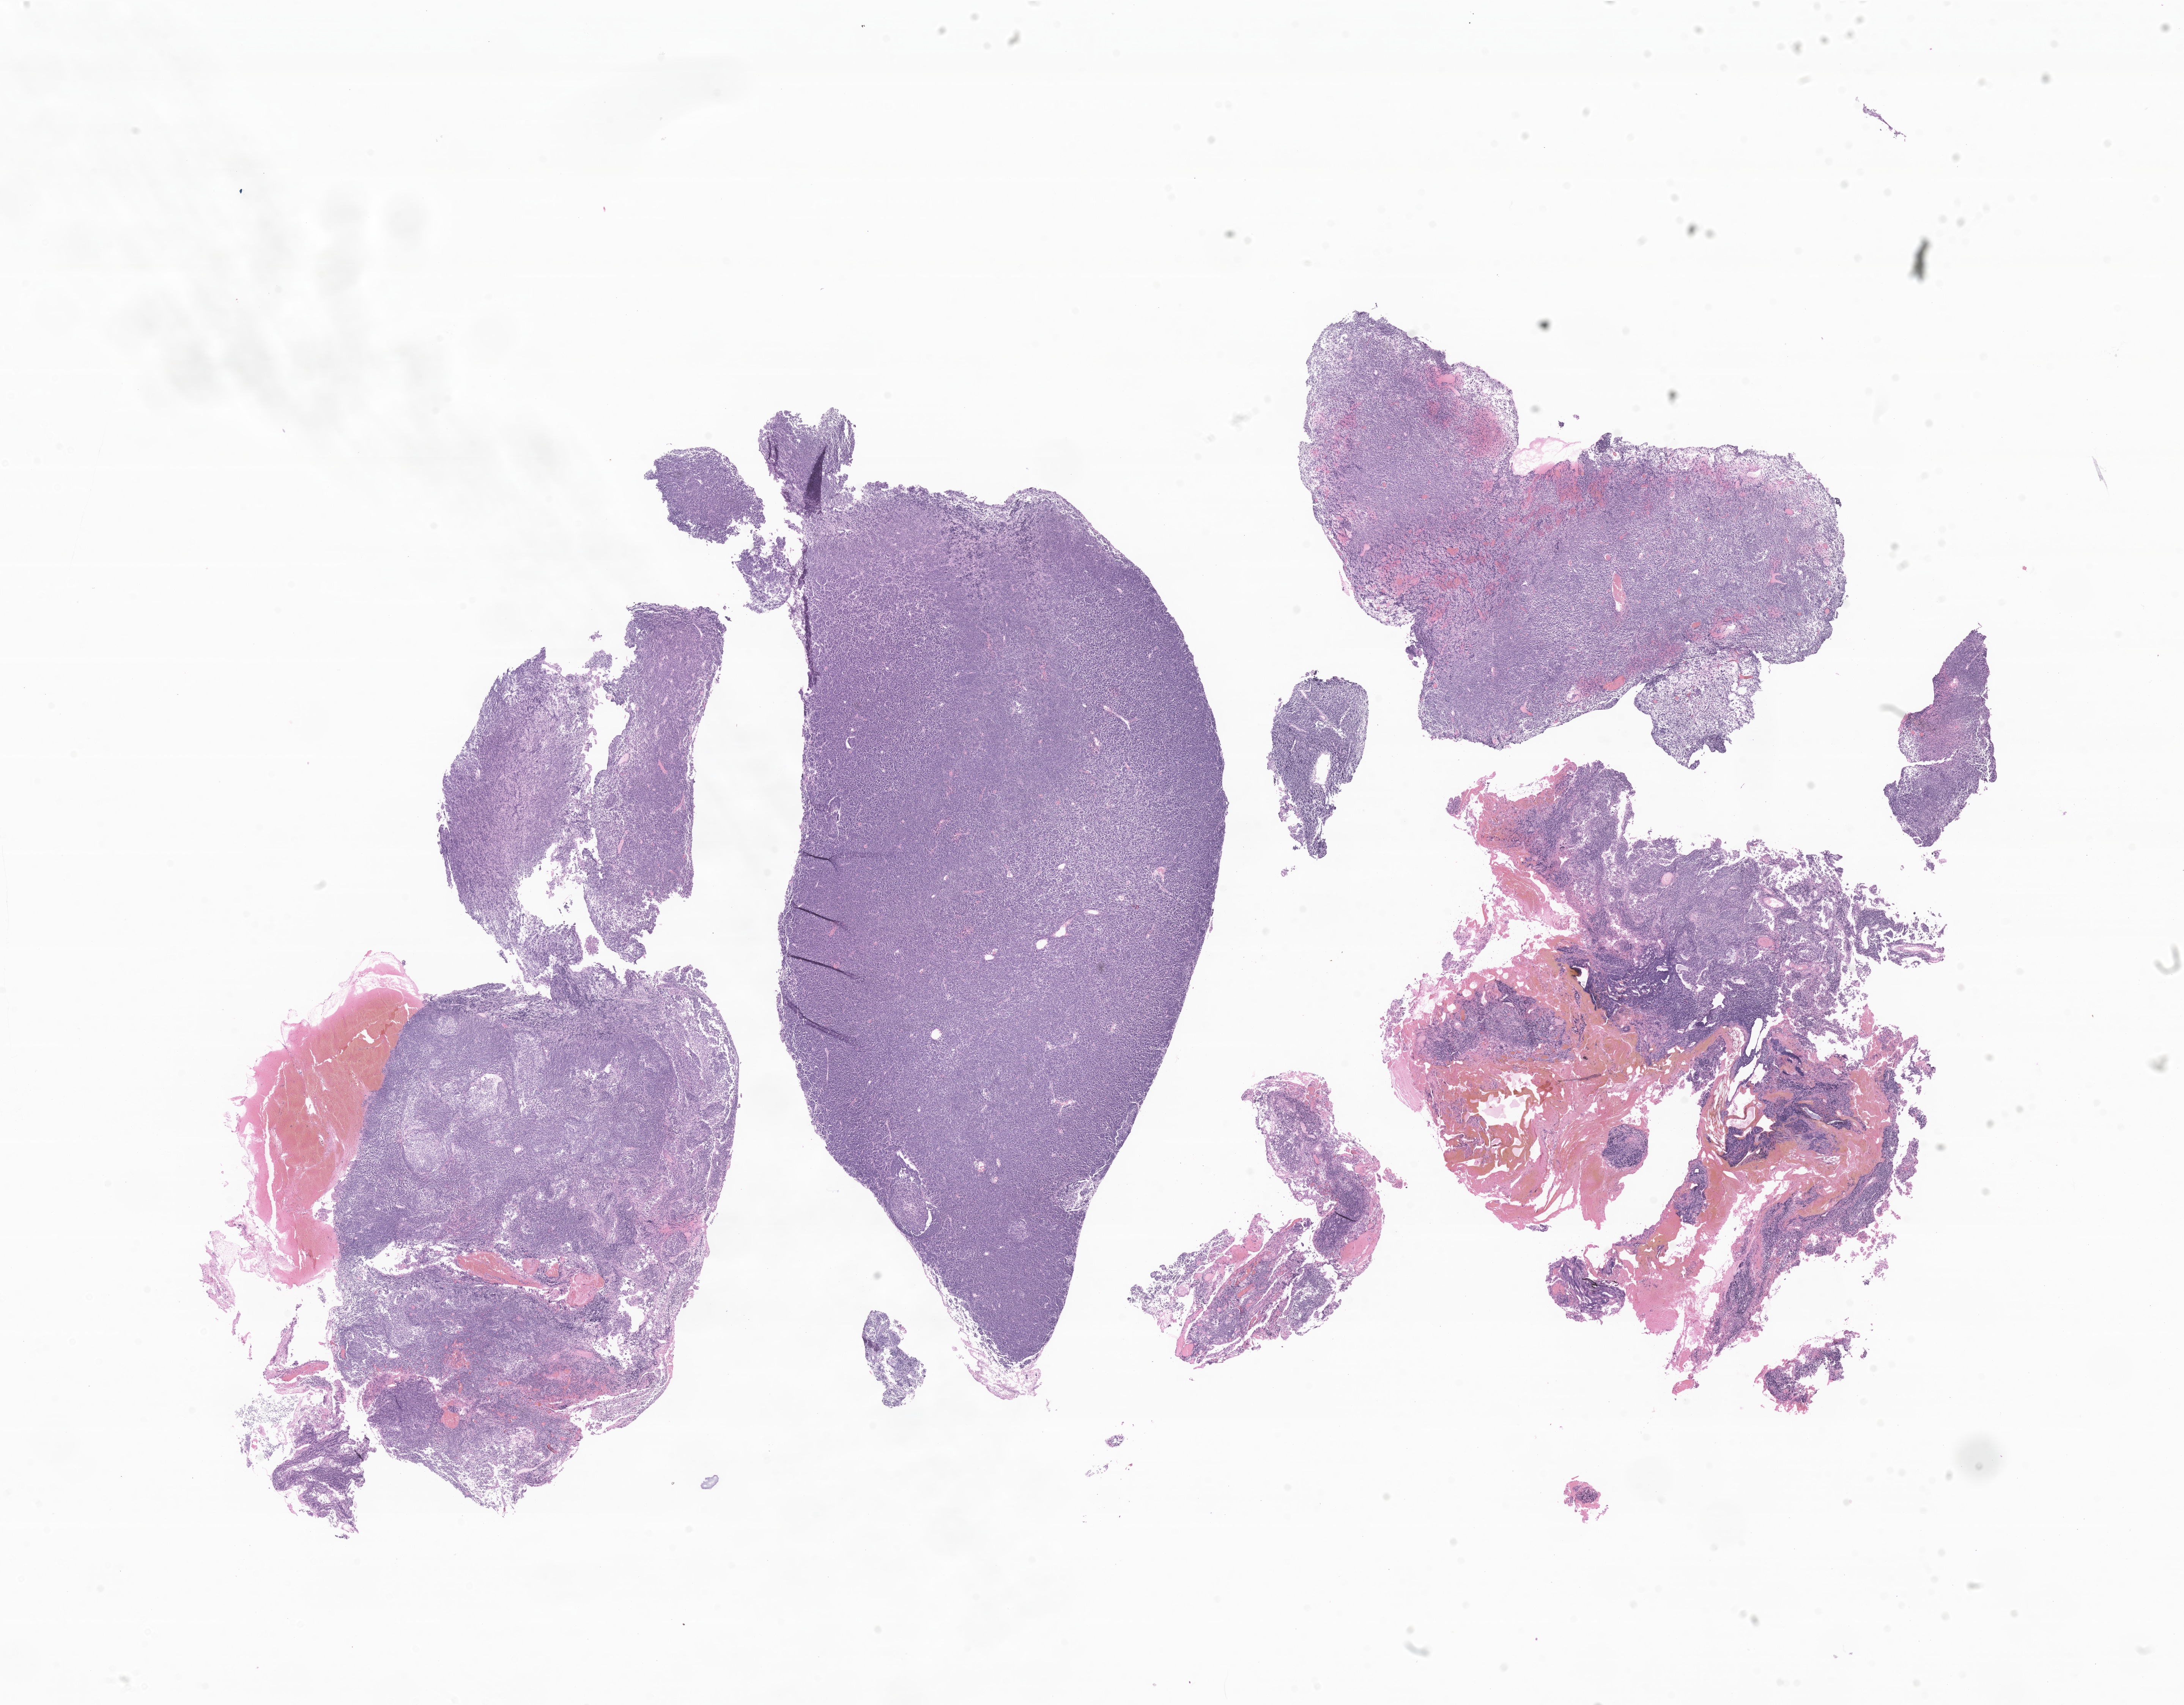
Whole-slide image, hematoxylin and eosin (H&E) stain of tumor tissue from the brain, whole scanned area (about 24.3 x 18.9 mm) shown as a low-resolution overview; formalin-fixed paraffin-embedded section. Patient female; age 833 days (about 2.3 years).
- recorded diagnosis: Medulloblastoma, NOS